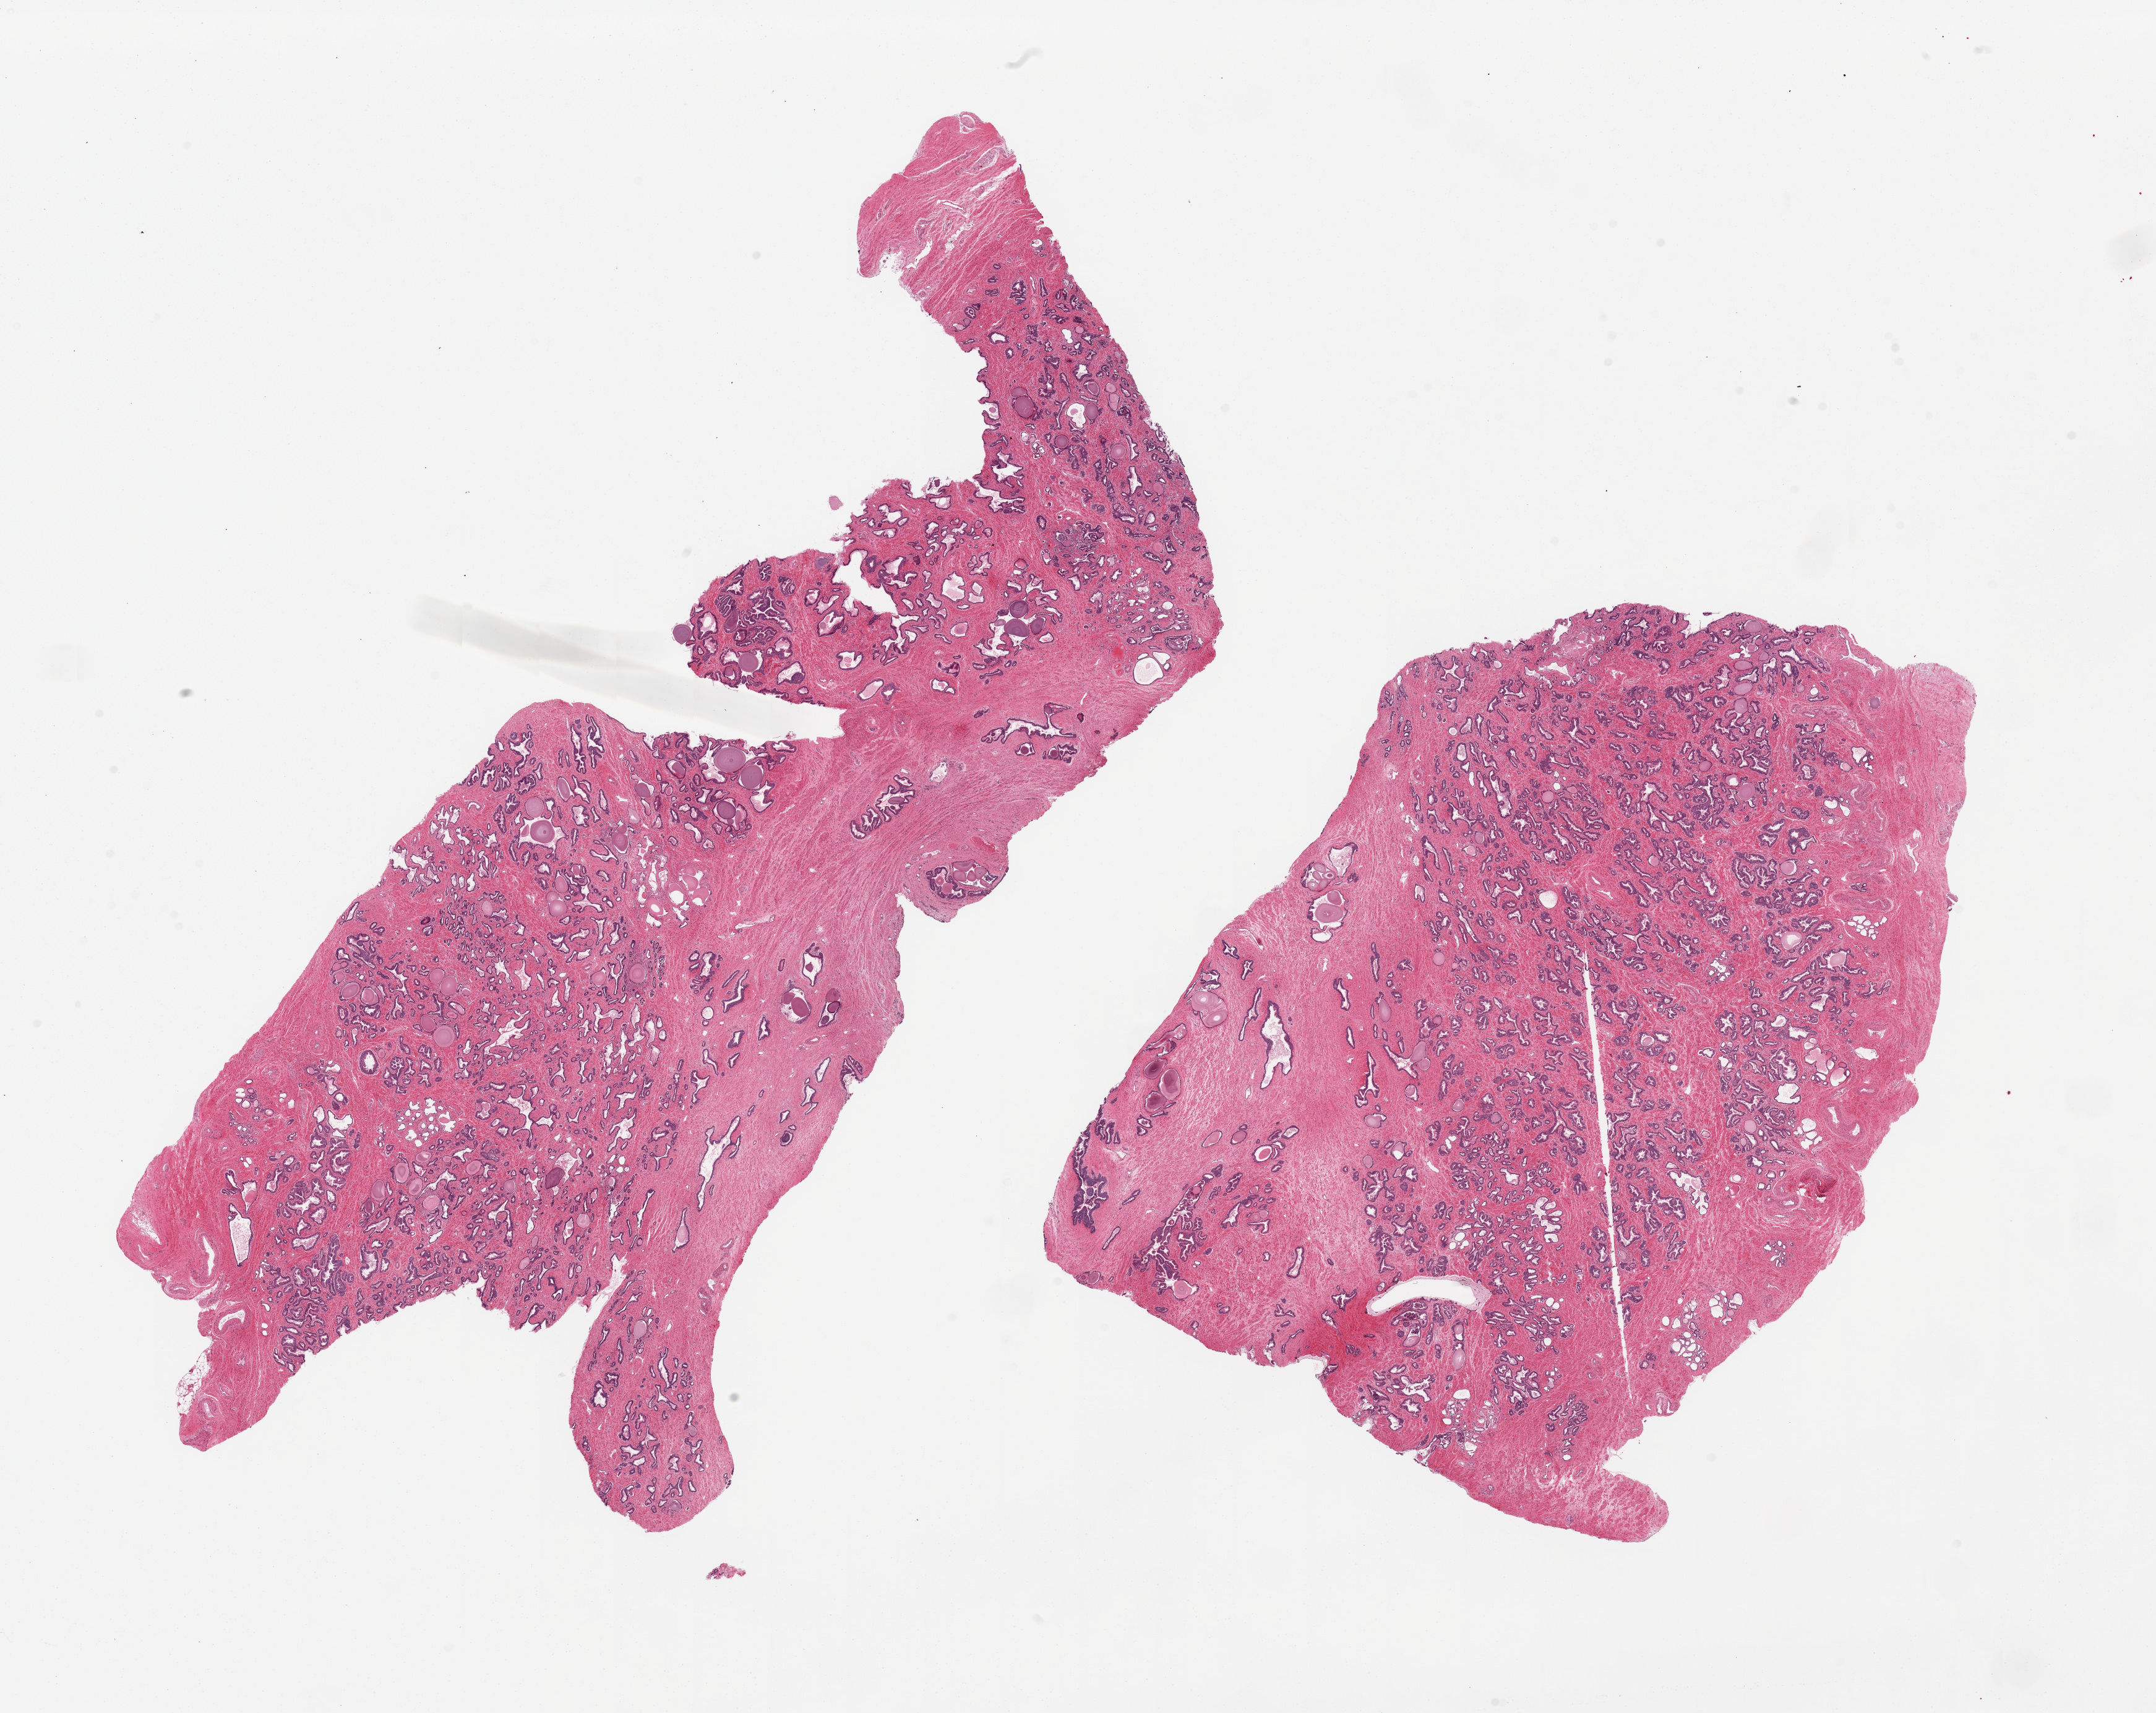
Whole-slide image, haematoxylin and eosin stain, a low-resolution overview of the entire scanned area, about 27.6 x 21.9 mm (slide scanned at 20x), PAXgene-fixed paraffin-embedded (PFPE) section, target tissue: prostate, tissue donor sample. Male donor.
• pathologist's review note for this sample: 2 pieces; stromal and glandular hyperplasia, some atrophy, focal chronic prostatitits, transitional metaplasia